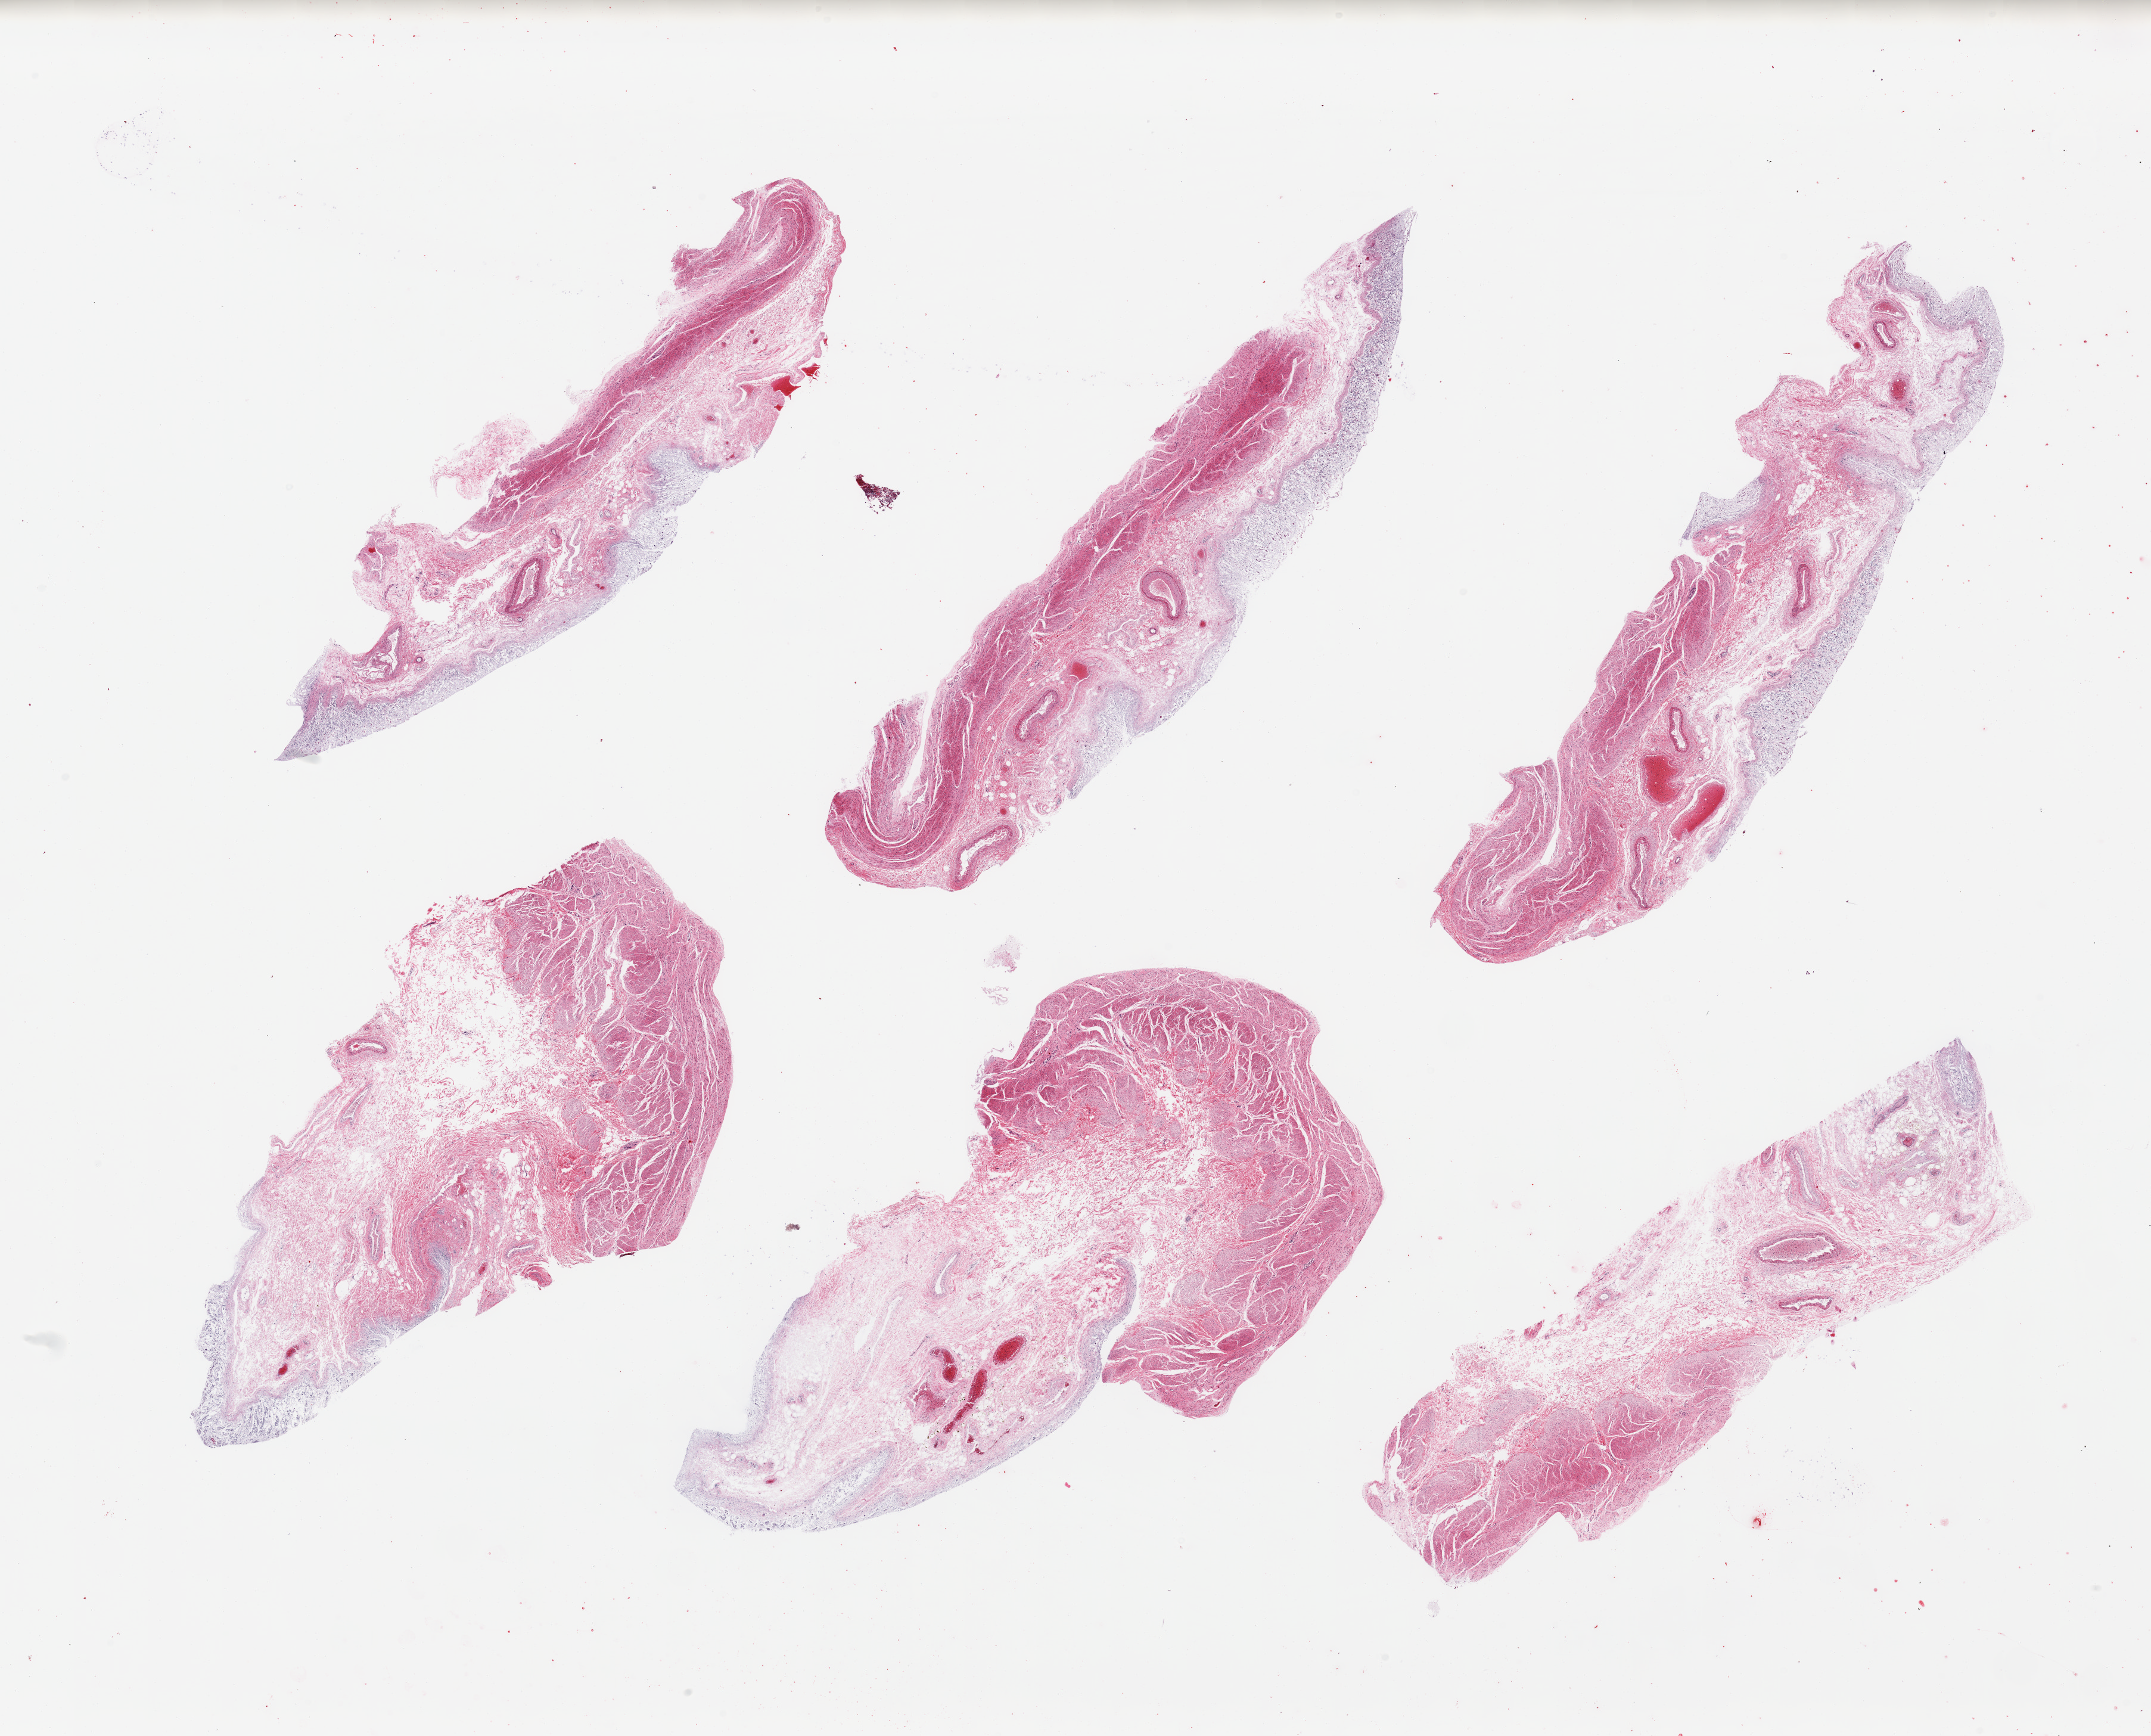
Whole-slide image, hematoxylin and eosin (H&E) stain — shown as a low-resolution overview of the whole scanned area (about 28.5 x 23.0 mm, slide scanned at 20x). PAXgene-fixed, paraffin-embedded tissue. Sampled site (target tissue): stomach. Tissue donor sample. Donor: female.
- review note (as recorded): 6 pieces; target mucosa up to ~0.6mm, advanced autolysis/sloughing